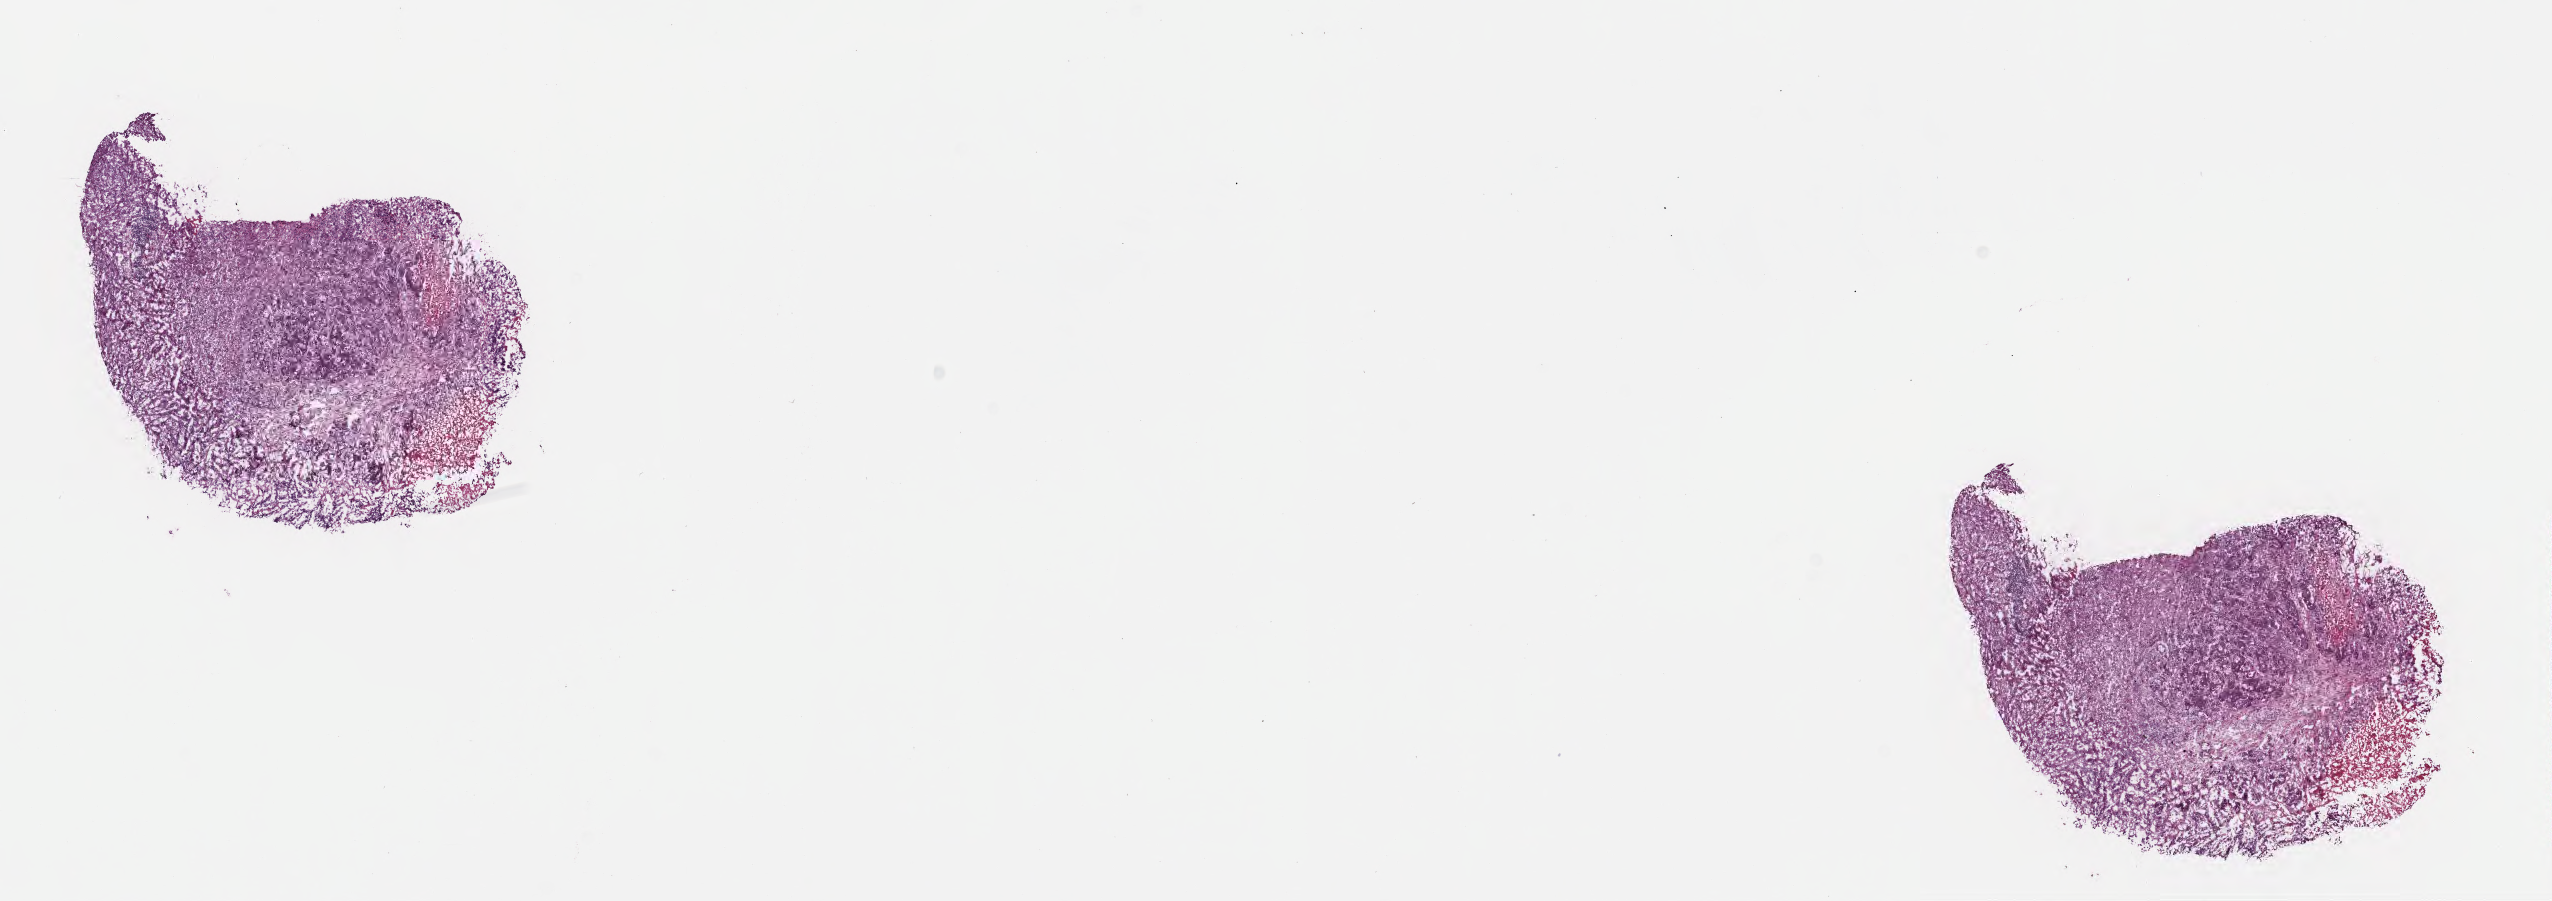
H&E whole-slide image, a low-resolution overview of the entire scanned area, about 20.6 x 7.3 mm. Frozen section (tissue freezing medium). Metastatic tumor tissue, resected from liver. Patient: male, age at initial diagnosis 59 years. Slide review estimates, as recorded: tumor cells 70%, tumor nuclei 80%, stromal cells 30%, necrosis 0%, normal cells 0%. Infiltration values recorded for this section: lymphocyte infiltration 0%, monocyte infiltration 0%, neutrophil infiltration 0%.
Section: top of the tissue portion. Patient diagnosis (primary): Adenocarcinoma, metastatic, NOS.